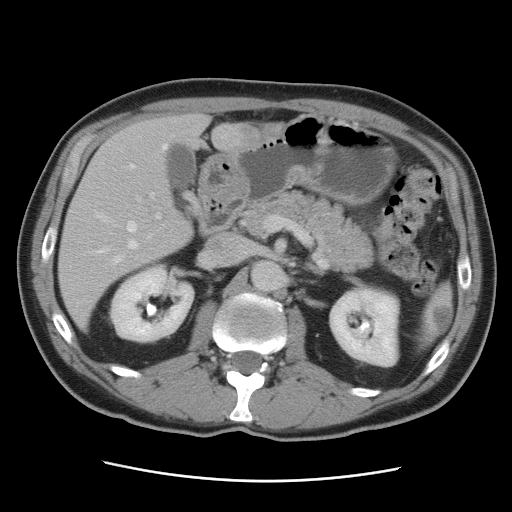
Contrast-enhanced abdominal CT, one axial slice. Slice 47 of 89 in the series (ordered by position). Soft-tissue window (W 400 / L 40 HU). 5 mm slice thickness. 512 × 512 image matrix. Male patient, age 59 years. Case-level facts recorded for this patient, not image findings: diagnosis: colorectal cancer liver metastases, imaged before liver resection; multiple liver metastases: yes.
Outlined on this slice (outlined manually by an expert reader):
- hepatic veins: bounding box (x1, y1, x2, y2) in pixels: (92, 136, 225, 263)
- liver: (59, 115, 284, 332)
- planned liver remnant (the part of the liver to remain after resection): (71, 115, 209, 245)
- portal vein (with intrahepatic branches): (136, 194, 161, 219)
- liver metastasis: (244, 127, 282, 142)